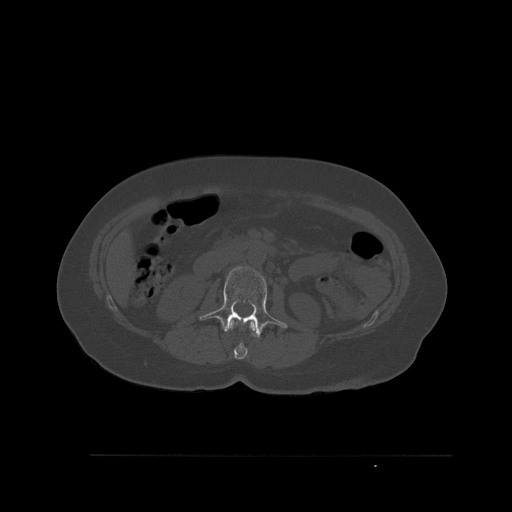
CT including the spine, one axial slice. Slice 248 of 527 in the series (ordered by position). Bone window (W 1800 / L 400 HU). 1.5 mm slice thickness. 512 × 512 image matrix, field of view 470 × 470 mm. Female patient, age 73 years. Case-level facts recorded for this patient, not image findings: primary cancer: breast.
Outlined on this slice (semi-automatic segmentation, software-assisted and operator-edited):
- L1 vertebra: bounding box [x1, y1, x2, y2] px = [229, 320, 256, 359]
- L2 vertebra: [199, 265, 288, 338]